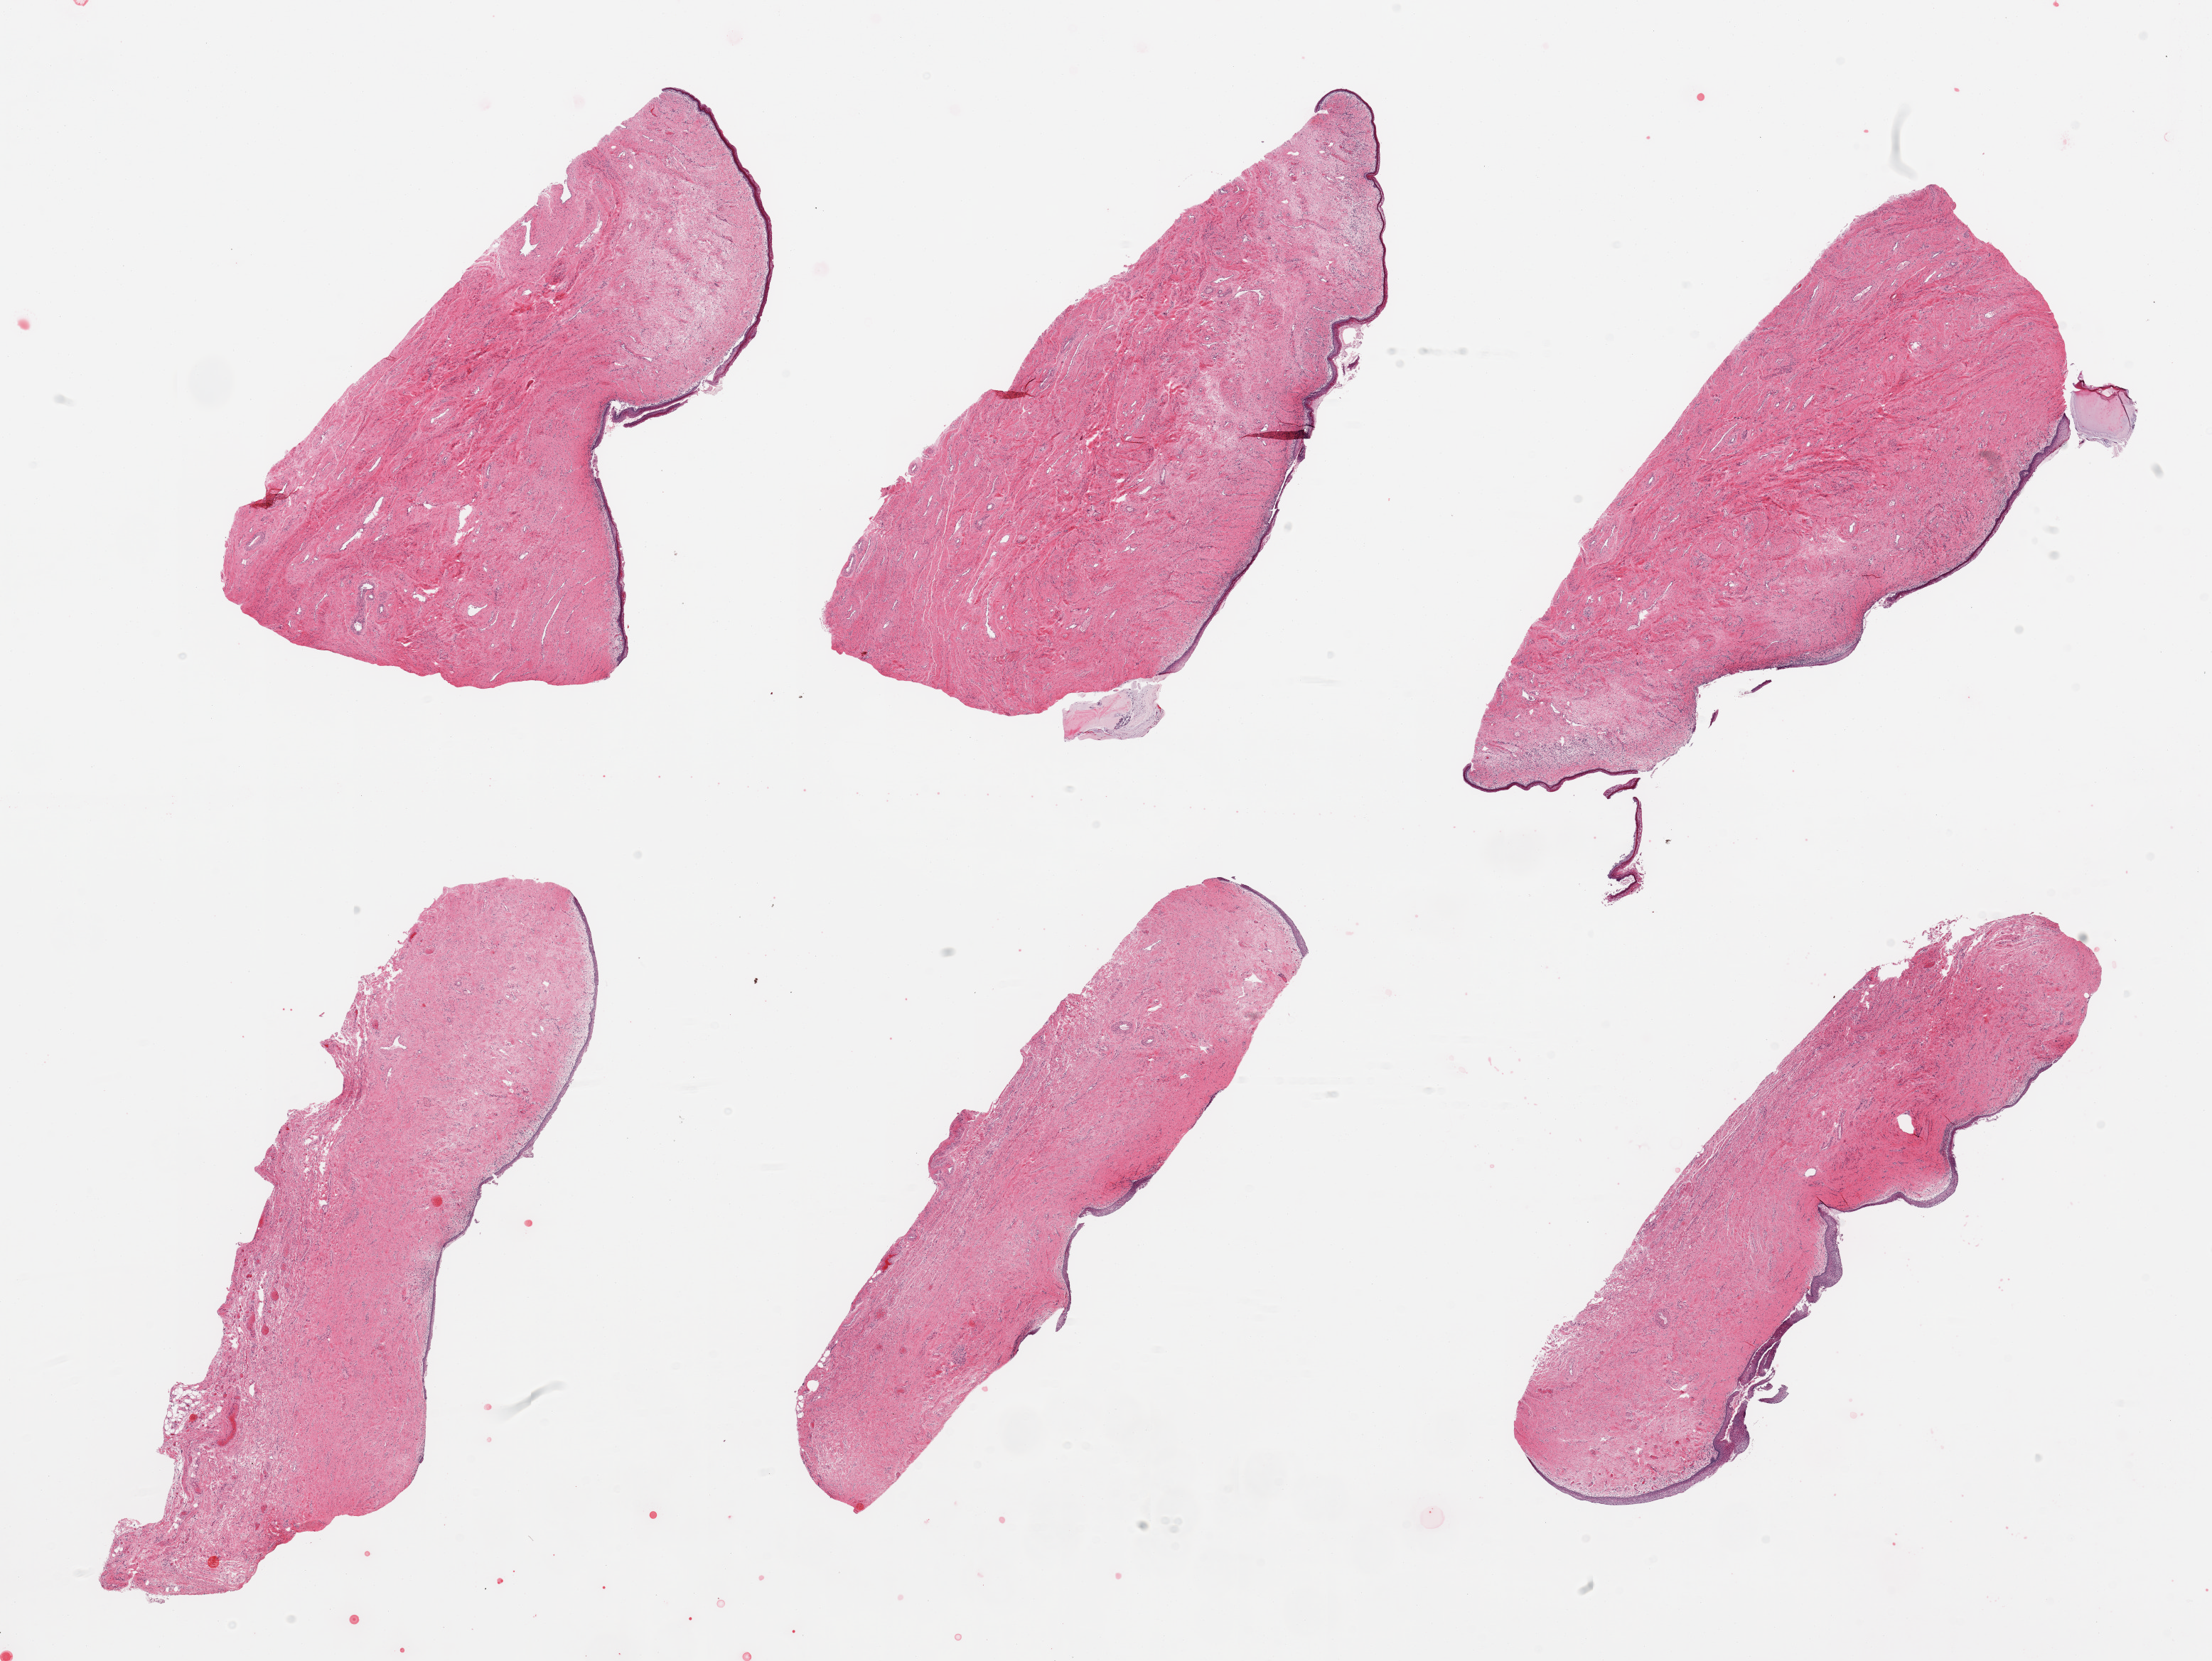
Hematoxylin and eosin (H&E) whole-slide image, whole scanned area (about 24.6 x 18.5 mm) shown as a low-resolution overview; PAXgene-fixed paraffin-embedded (PFPE) section; section of vagina (target tissue); tissue donor sample.
* pathologist's review note for this sample: 6 pieces, squamous mucosa atrophic, moderately sloughed